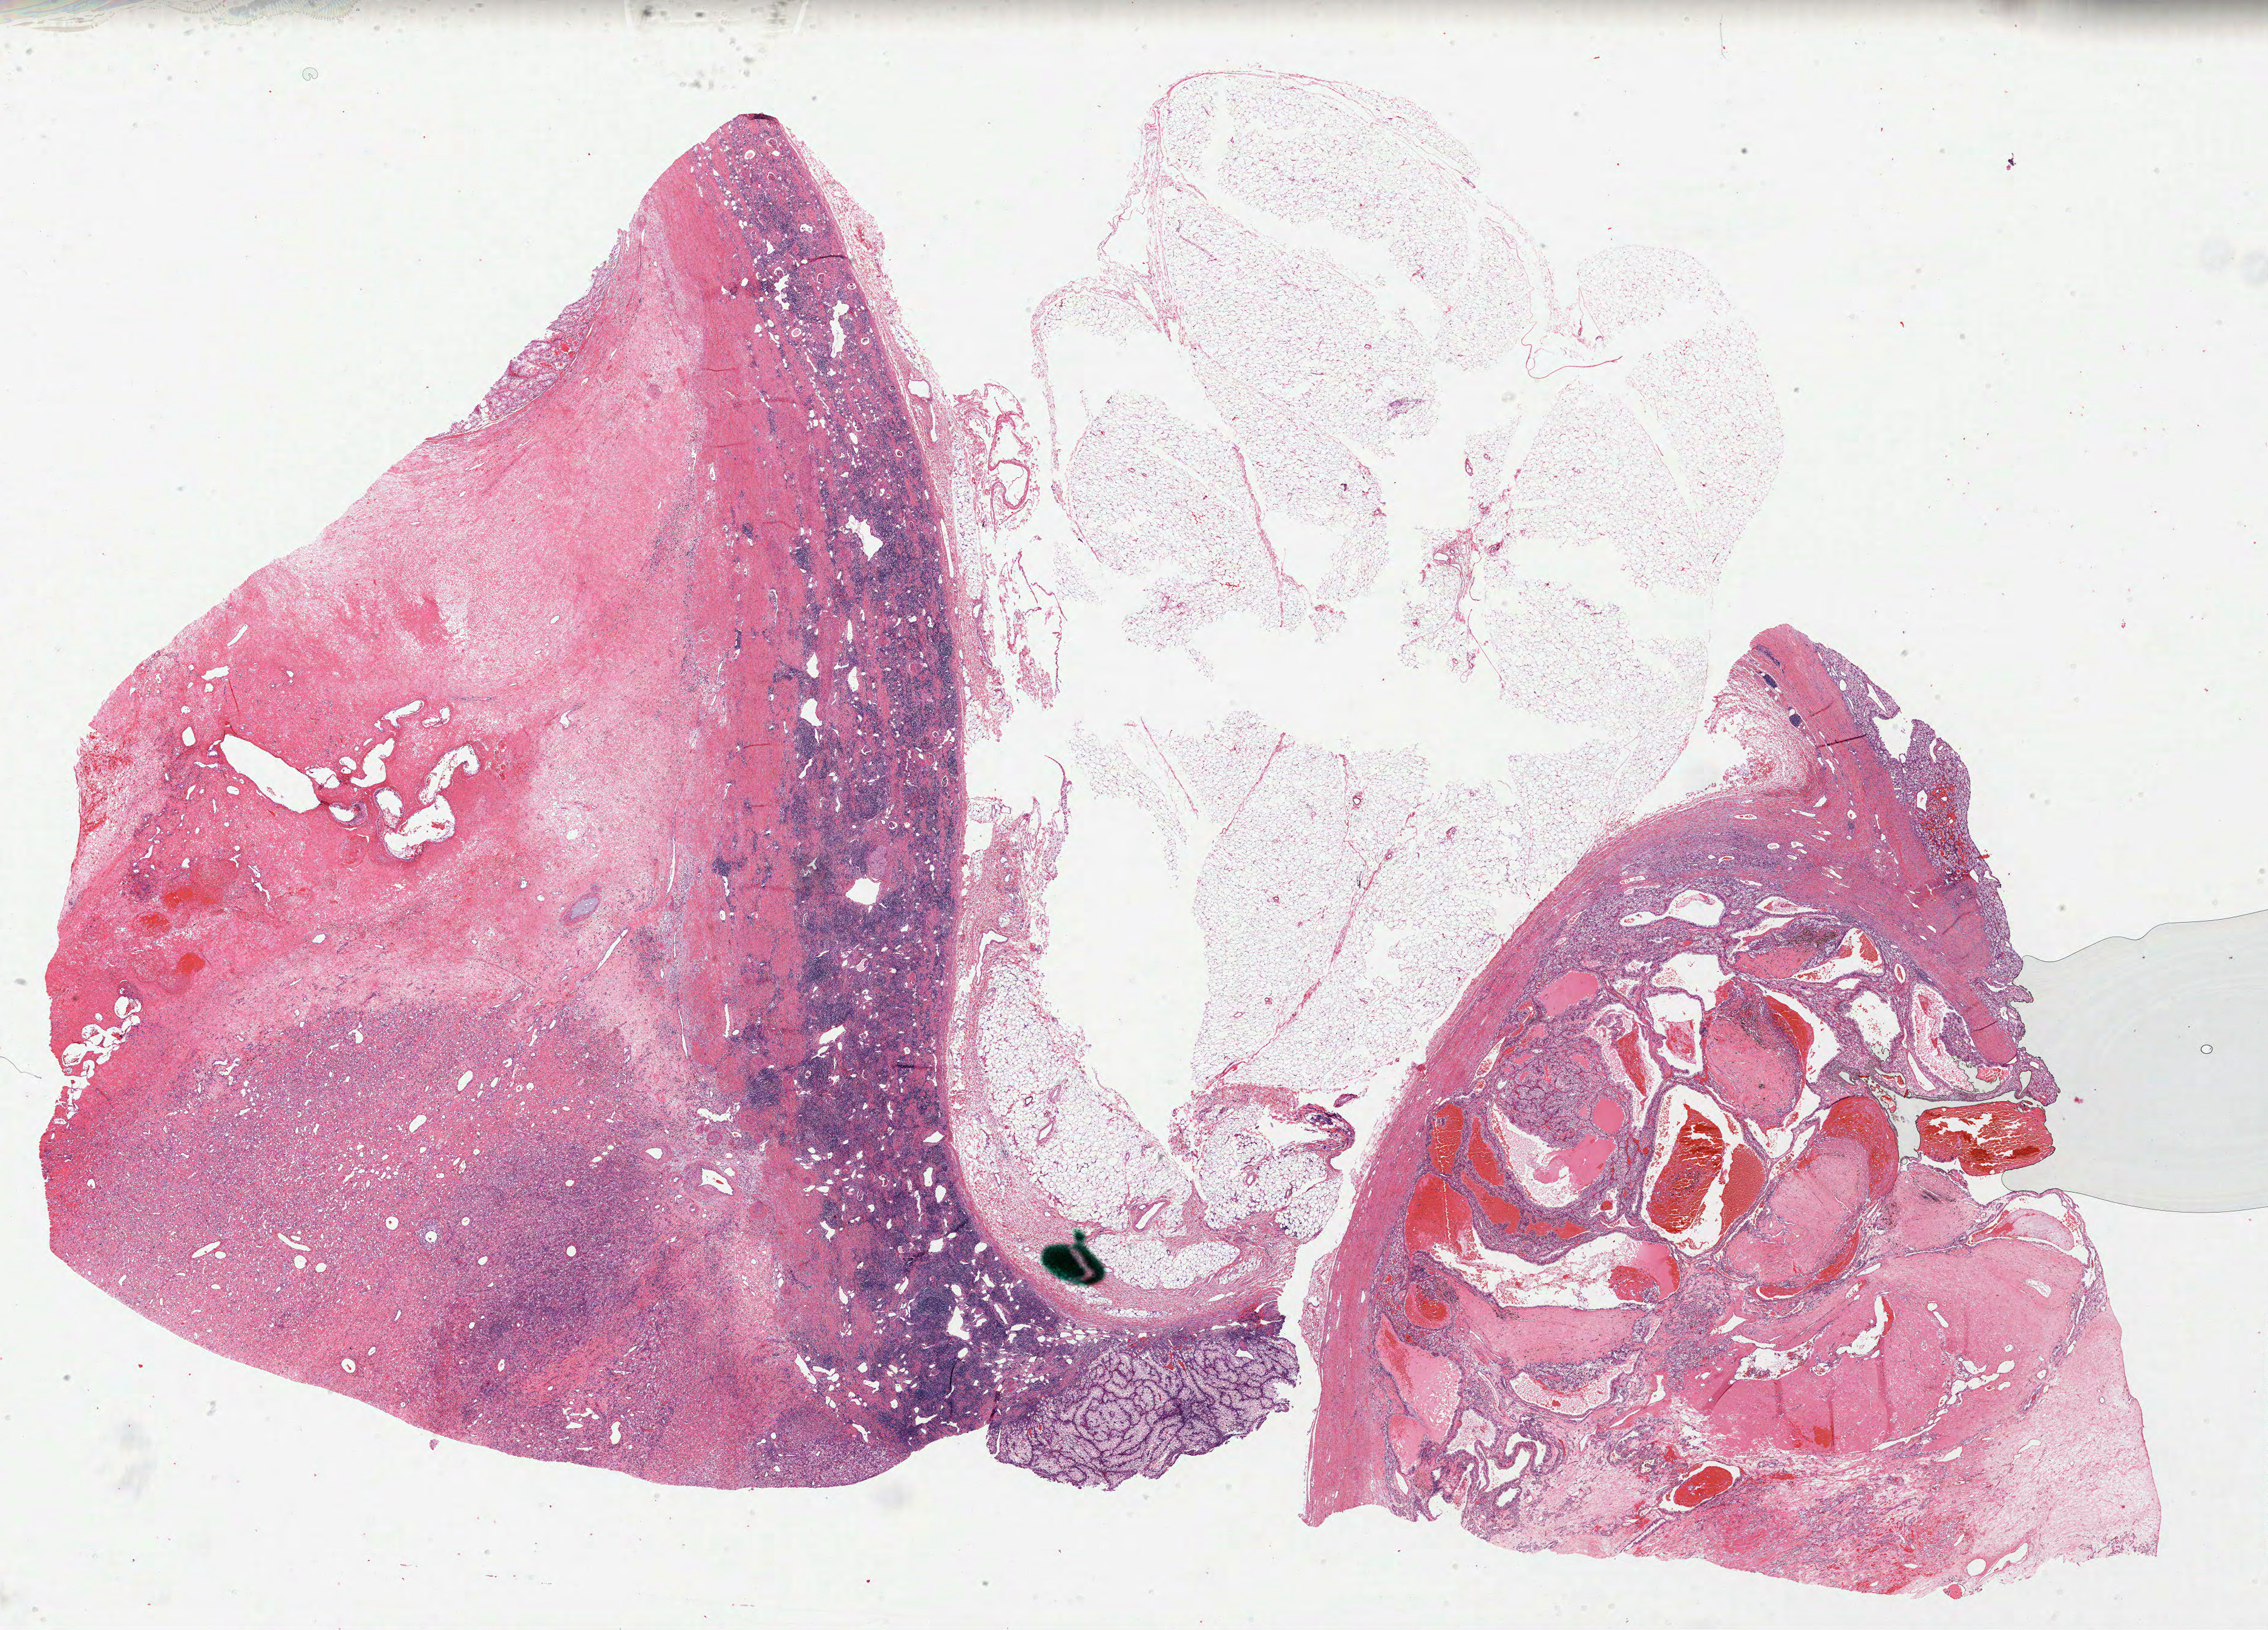
Hematoxylin and eosin (H&E) stained whole-slide image — low-resolution overview of the scanned area, about 30.2 x 21.7 mm. FFPE section. Sample: primary tumour, kidney. Male patient; age at initial diagnosis 43 years. Histologic grade: G3 (poorly differentiated).
AJCC pathologic stage: III (6th edition). Diagnosis: Clear cell adenocarcinoma, NOS. Laterality: right.